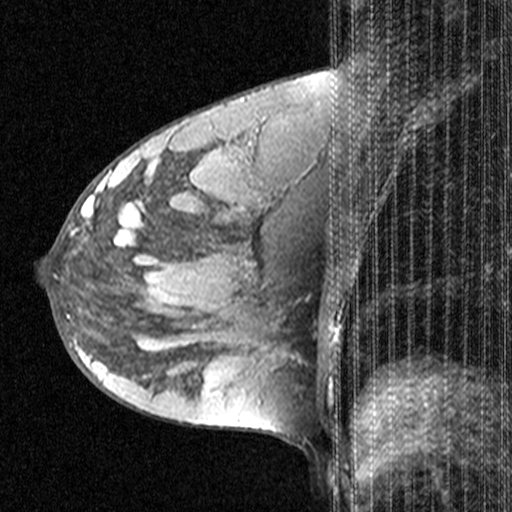
Breast MRI (dynamic contrast-enhanced), one sagittal slice. Position 22 of 44 along the scan axis. Dynamic contrast-enhanced study with each time point stored as its own series, time point 2 of 3 at this slice position (early post-contrast, ordered by acquisition time). 1.5 T. TE 4.5 ms, TR 11 ms. 512 × 512 image matrix, field of view 200 × 200 mm. Patient: female, 28 years. Case-level facts recorded for this patient, not image findings: setting: breast cancer imaged before/during neoadjuvant chemotherapy; receptor status: HR-positive, HER2-negative.
Outlined on this slice (semi-automatic segmentation, software-assisted and operator-edited):
- analysis volume of interest (the breast-tissue region the enhancement analysis was run in; not a lesion): box from (x=48, y=182) to (x=151, y=283) px
- tumour enhancement mask (voxels above the 90 % enhancement threshold inside the analysis volume of interest): (x=86, y=182)–(x=102, y=223)